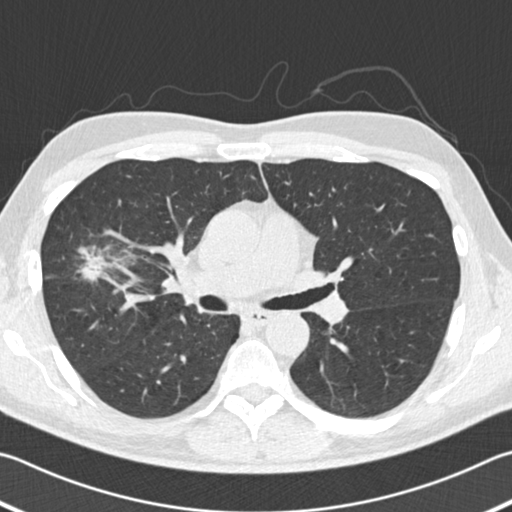
Low-dose screening chest CT, axial slice; second screening round (one year after baseline); lung window (W 1500 / L -600 HU); 120 kVp; slice 70 of 182 in the series. Male participant, aged 56 years at enrolment.
Expert-annotated lung lesion, bounding box <50,234,138,299> (left, top, right, bottom; pixels). Reader record for this screening exam (exam-level; its link to the box is not recorded): non-calcified nodule or mass ≥4 mm, right upper lobe, 18 × 14 mm, spiculated (stellate) margins, soft tissue attenuation, pre-existing on the prior screen: yes; interval growth: yes. Later outcome: lung cancer diagnosed 42 days after this screen — bronchiolo-alveolar adenocarcinoma, NOS, right upper lobe, well differentiated (G1), stage IIB (AJCC 6th edition), 30 mm at pathology.